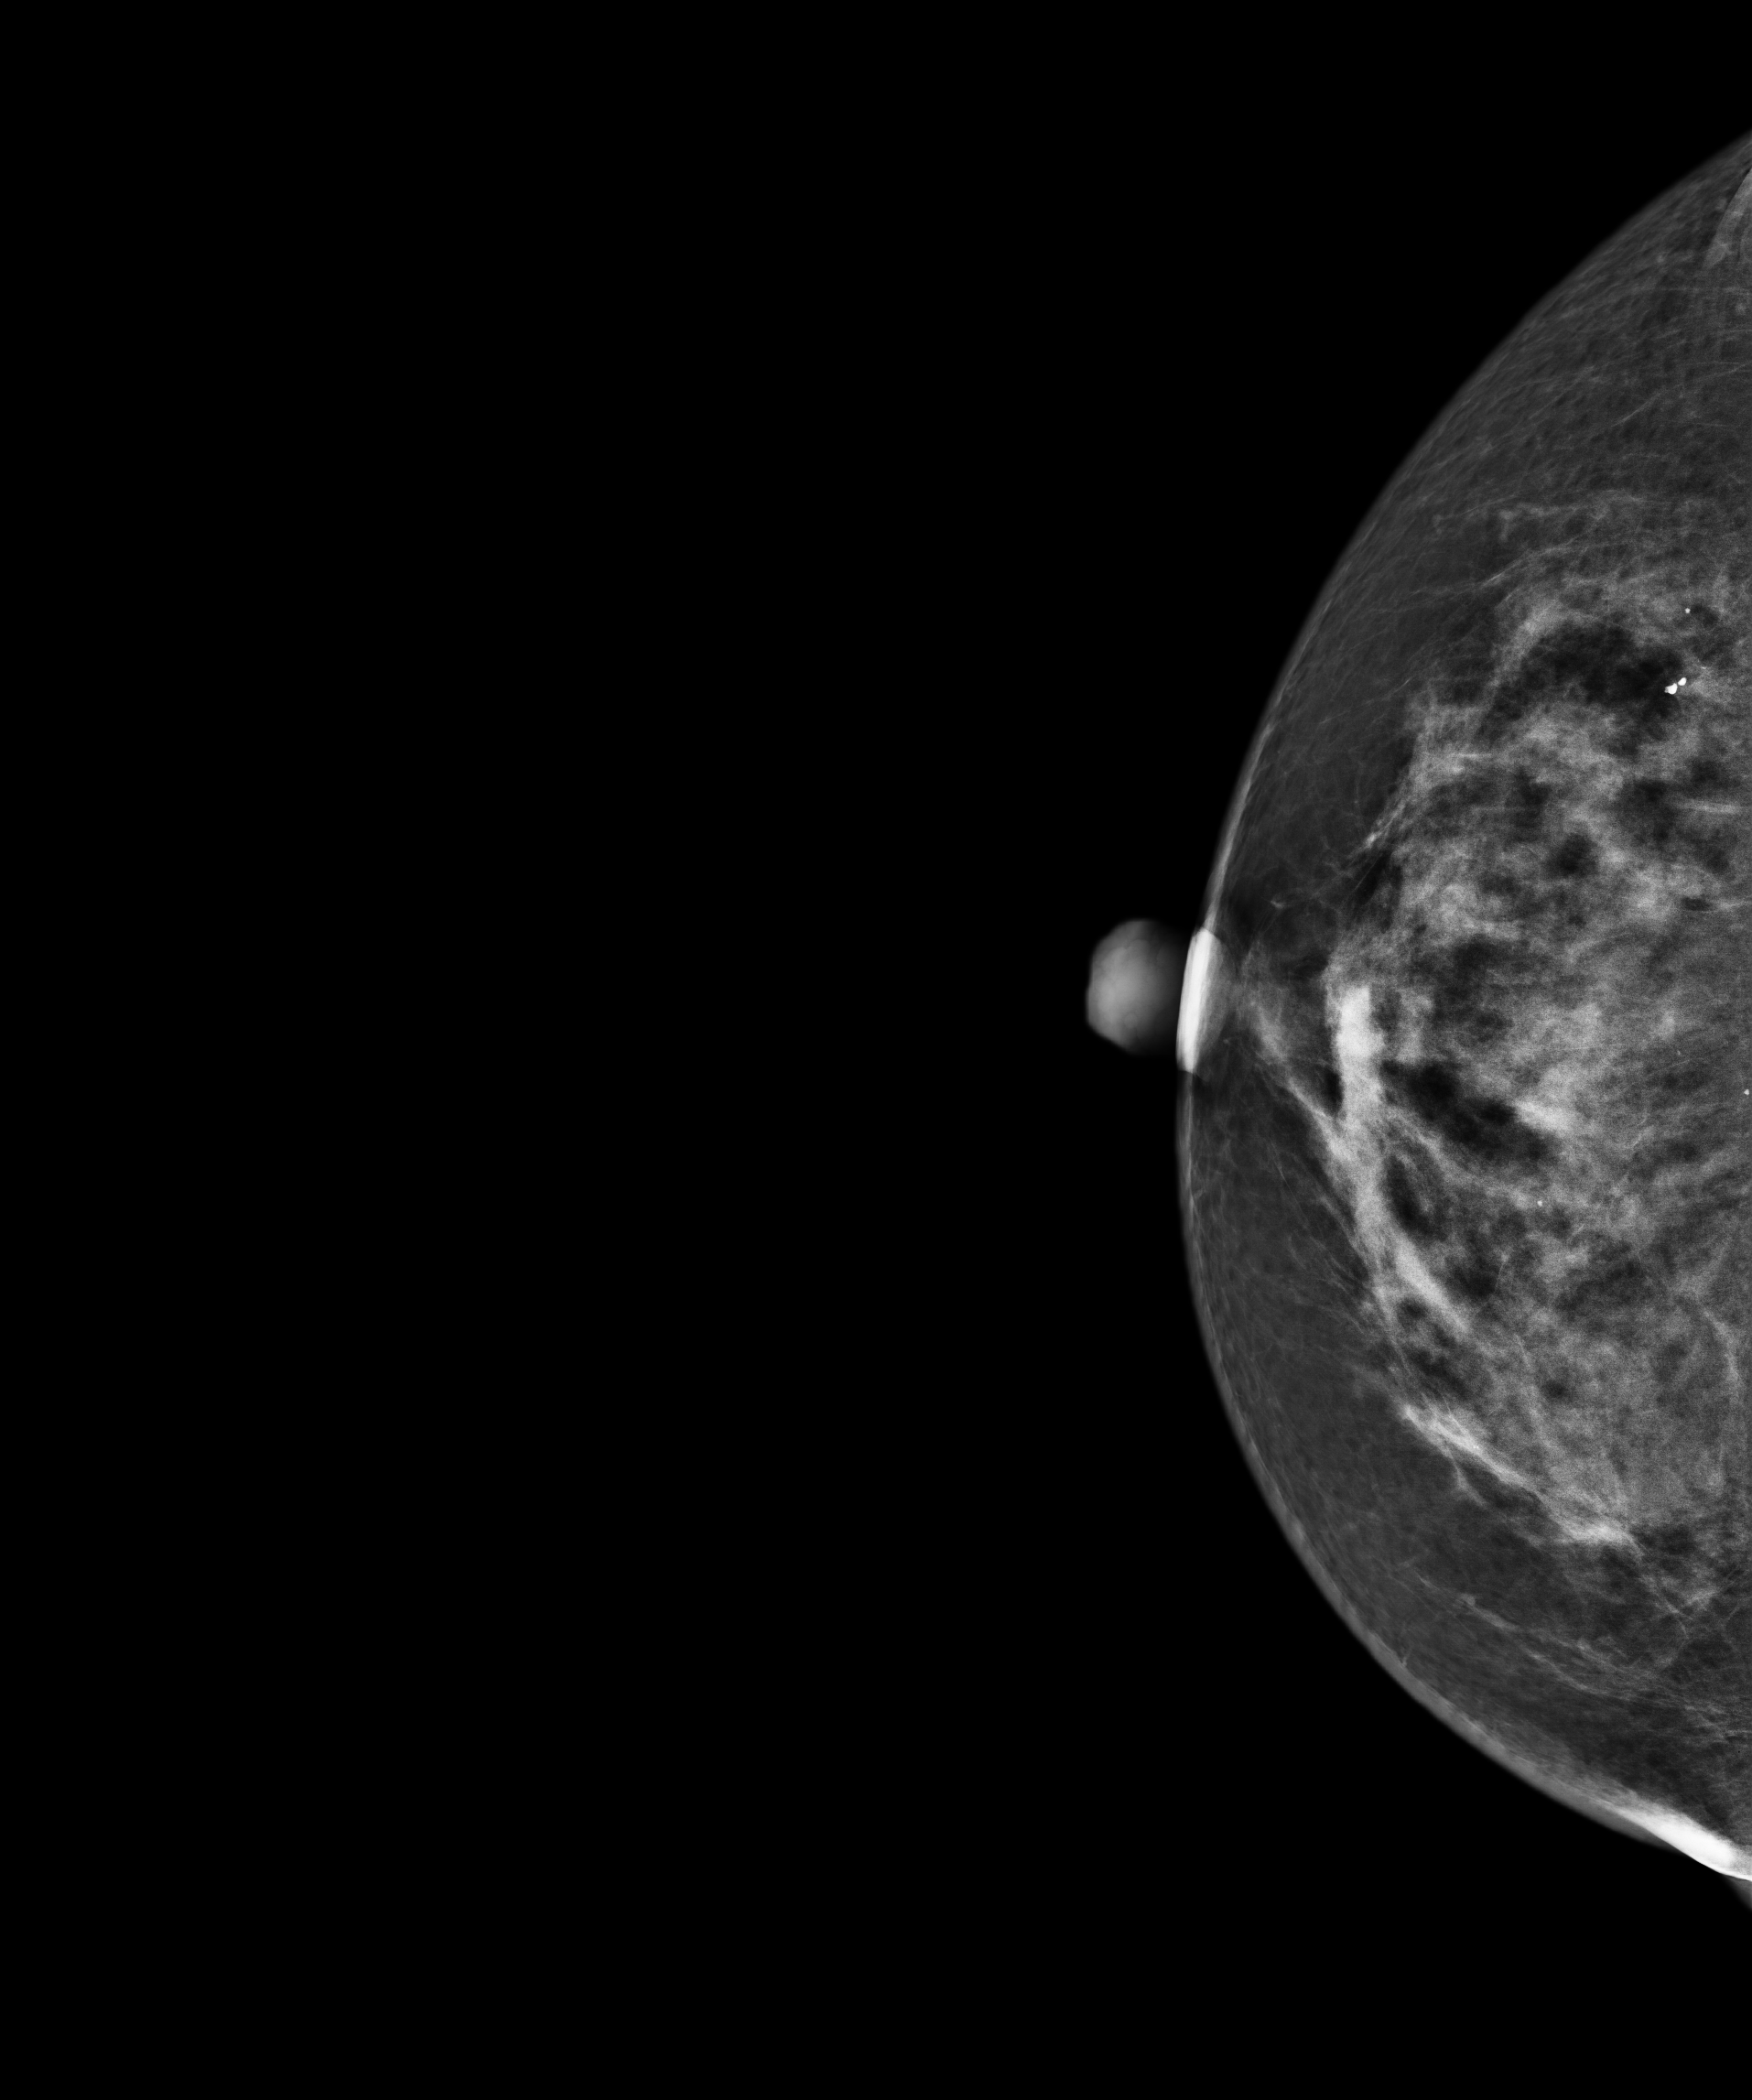
Annual screening mammography examination; compressed breast thickness 65.4 mm; system: Senographe Pristina.
Image type: full-field digital mammogram. Breast: right. Projection: craniocaudal (CC) view.